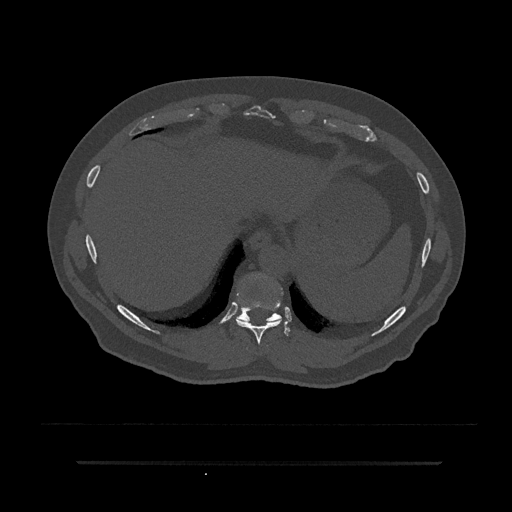
CT including the spine, one axial slice; slice 357 of 797 in the series (ordered by position); 120 kVp; bone window (W 1800 / L 400 HU); 0.5 mm slice thickness; 512 × 512 image matrix, field of view 464 × 464 mm. Patient: male, 59 years. Case-level facts recorded for this patient, not image findings: primary cancer: bile ducts; vertebrae with lytic lesions (as recorded): T10.
Structures marked on this image (semi-automatically segmented with operator editing):
- T10 vertebra: bounding box <236,275,290,336> (left, top, right, bottom; pixels)
- T9 vertebra: <236,301,282,345>